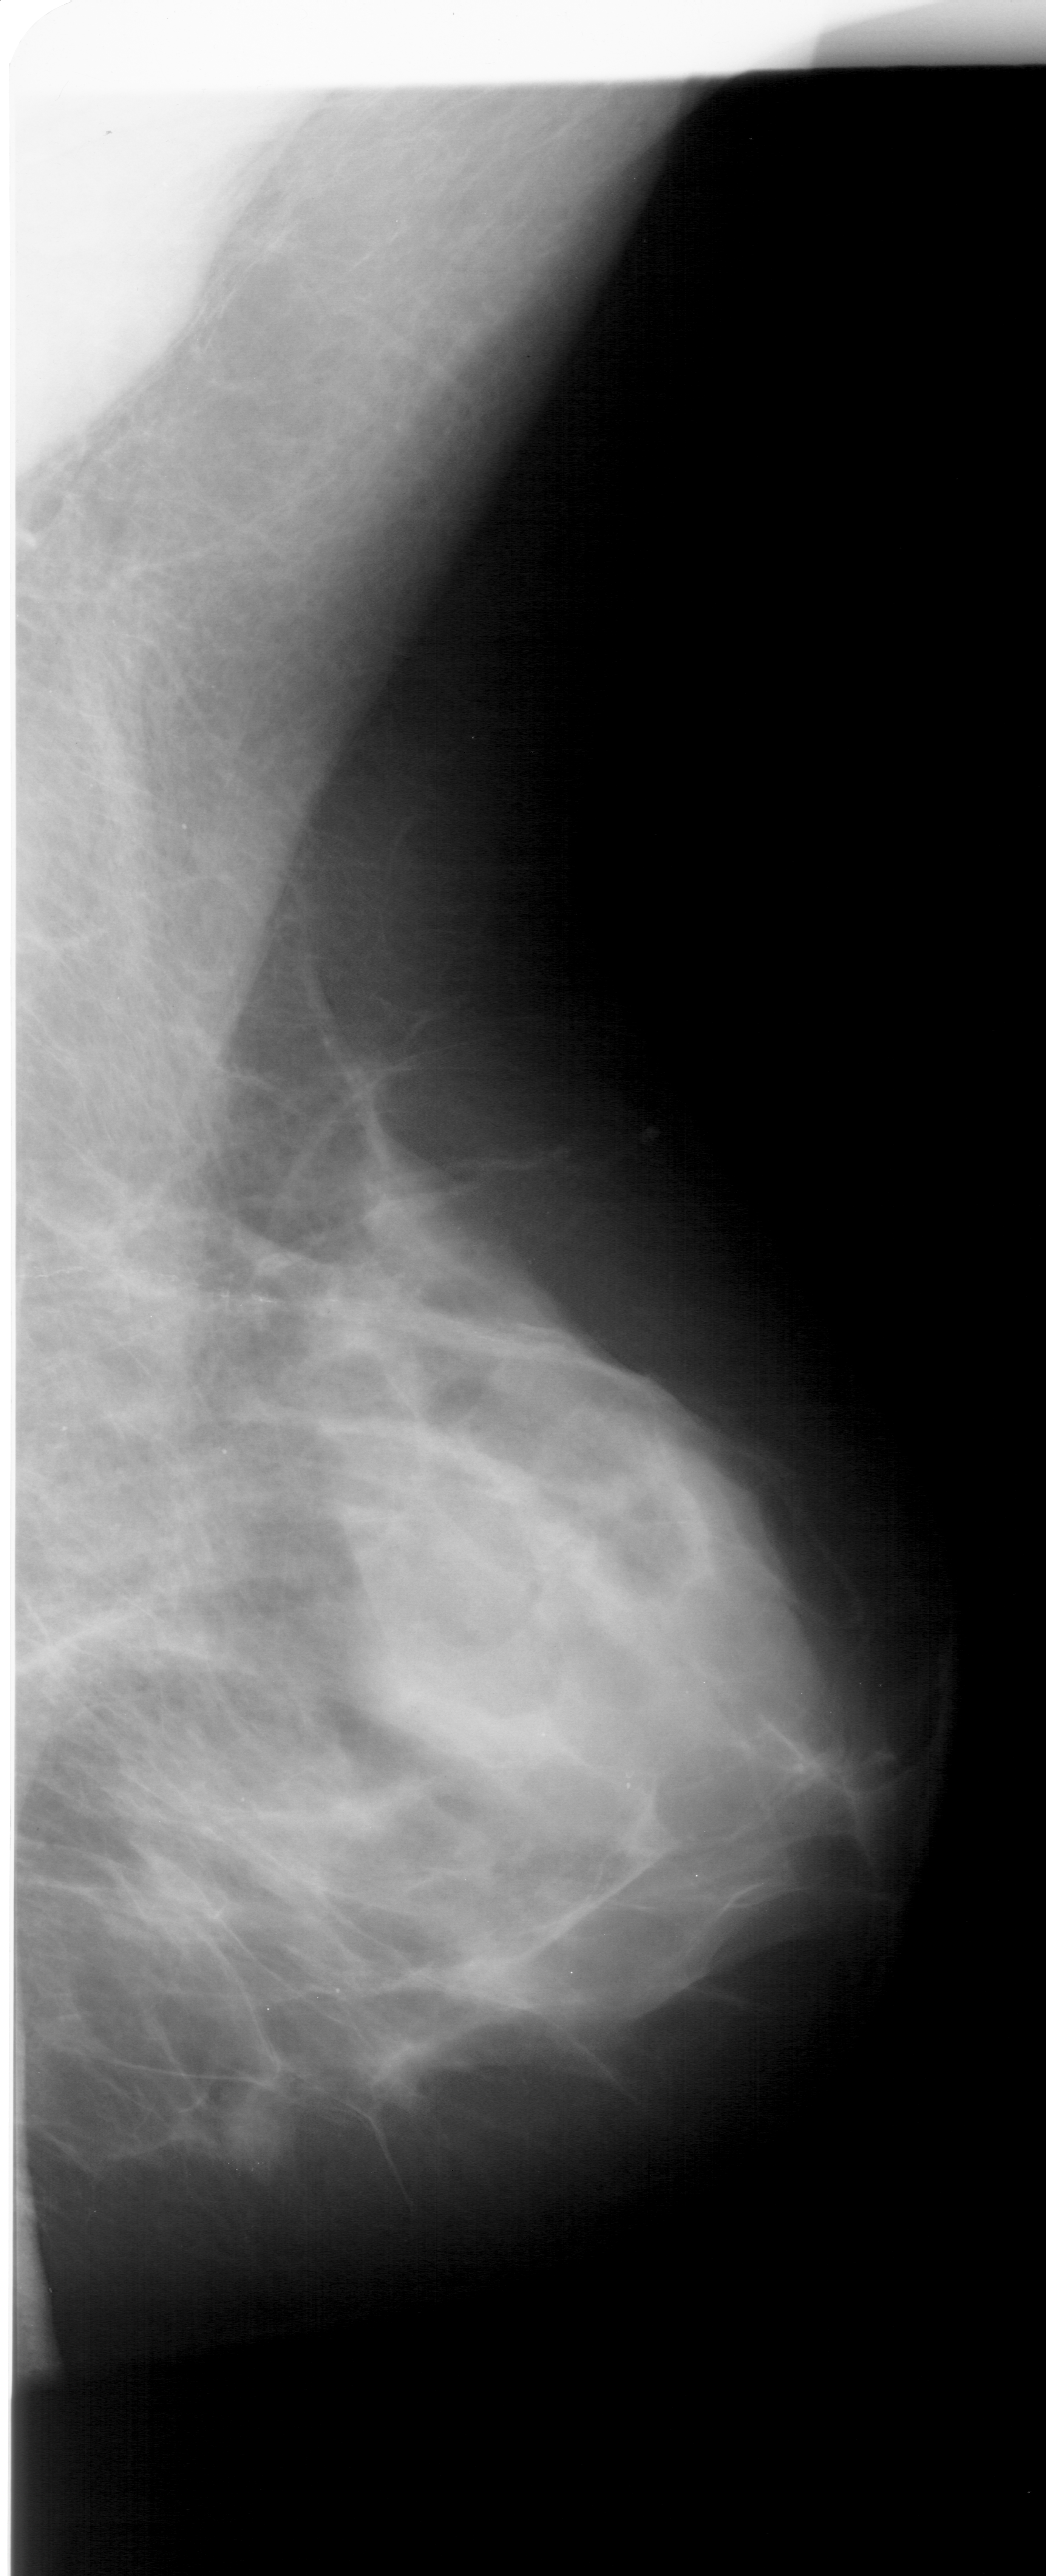
Scanned film-screen mammogram, right breast, MLO view.
- Finding: mass, shape lobulated, margins circumscribed; BI-RADS assessment category 4; pathology (as recorded): benign.